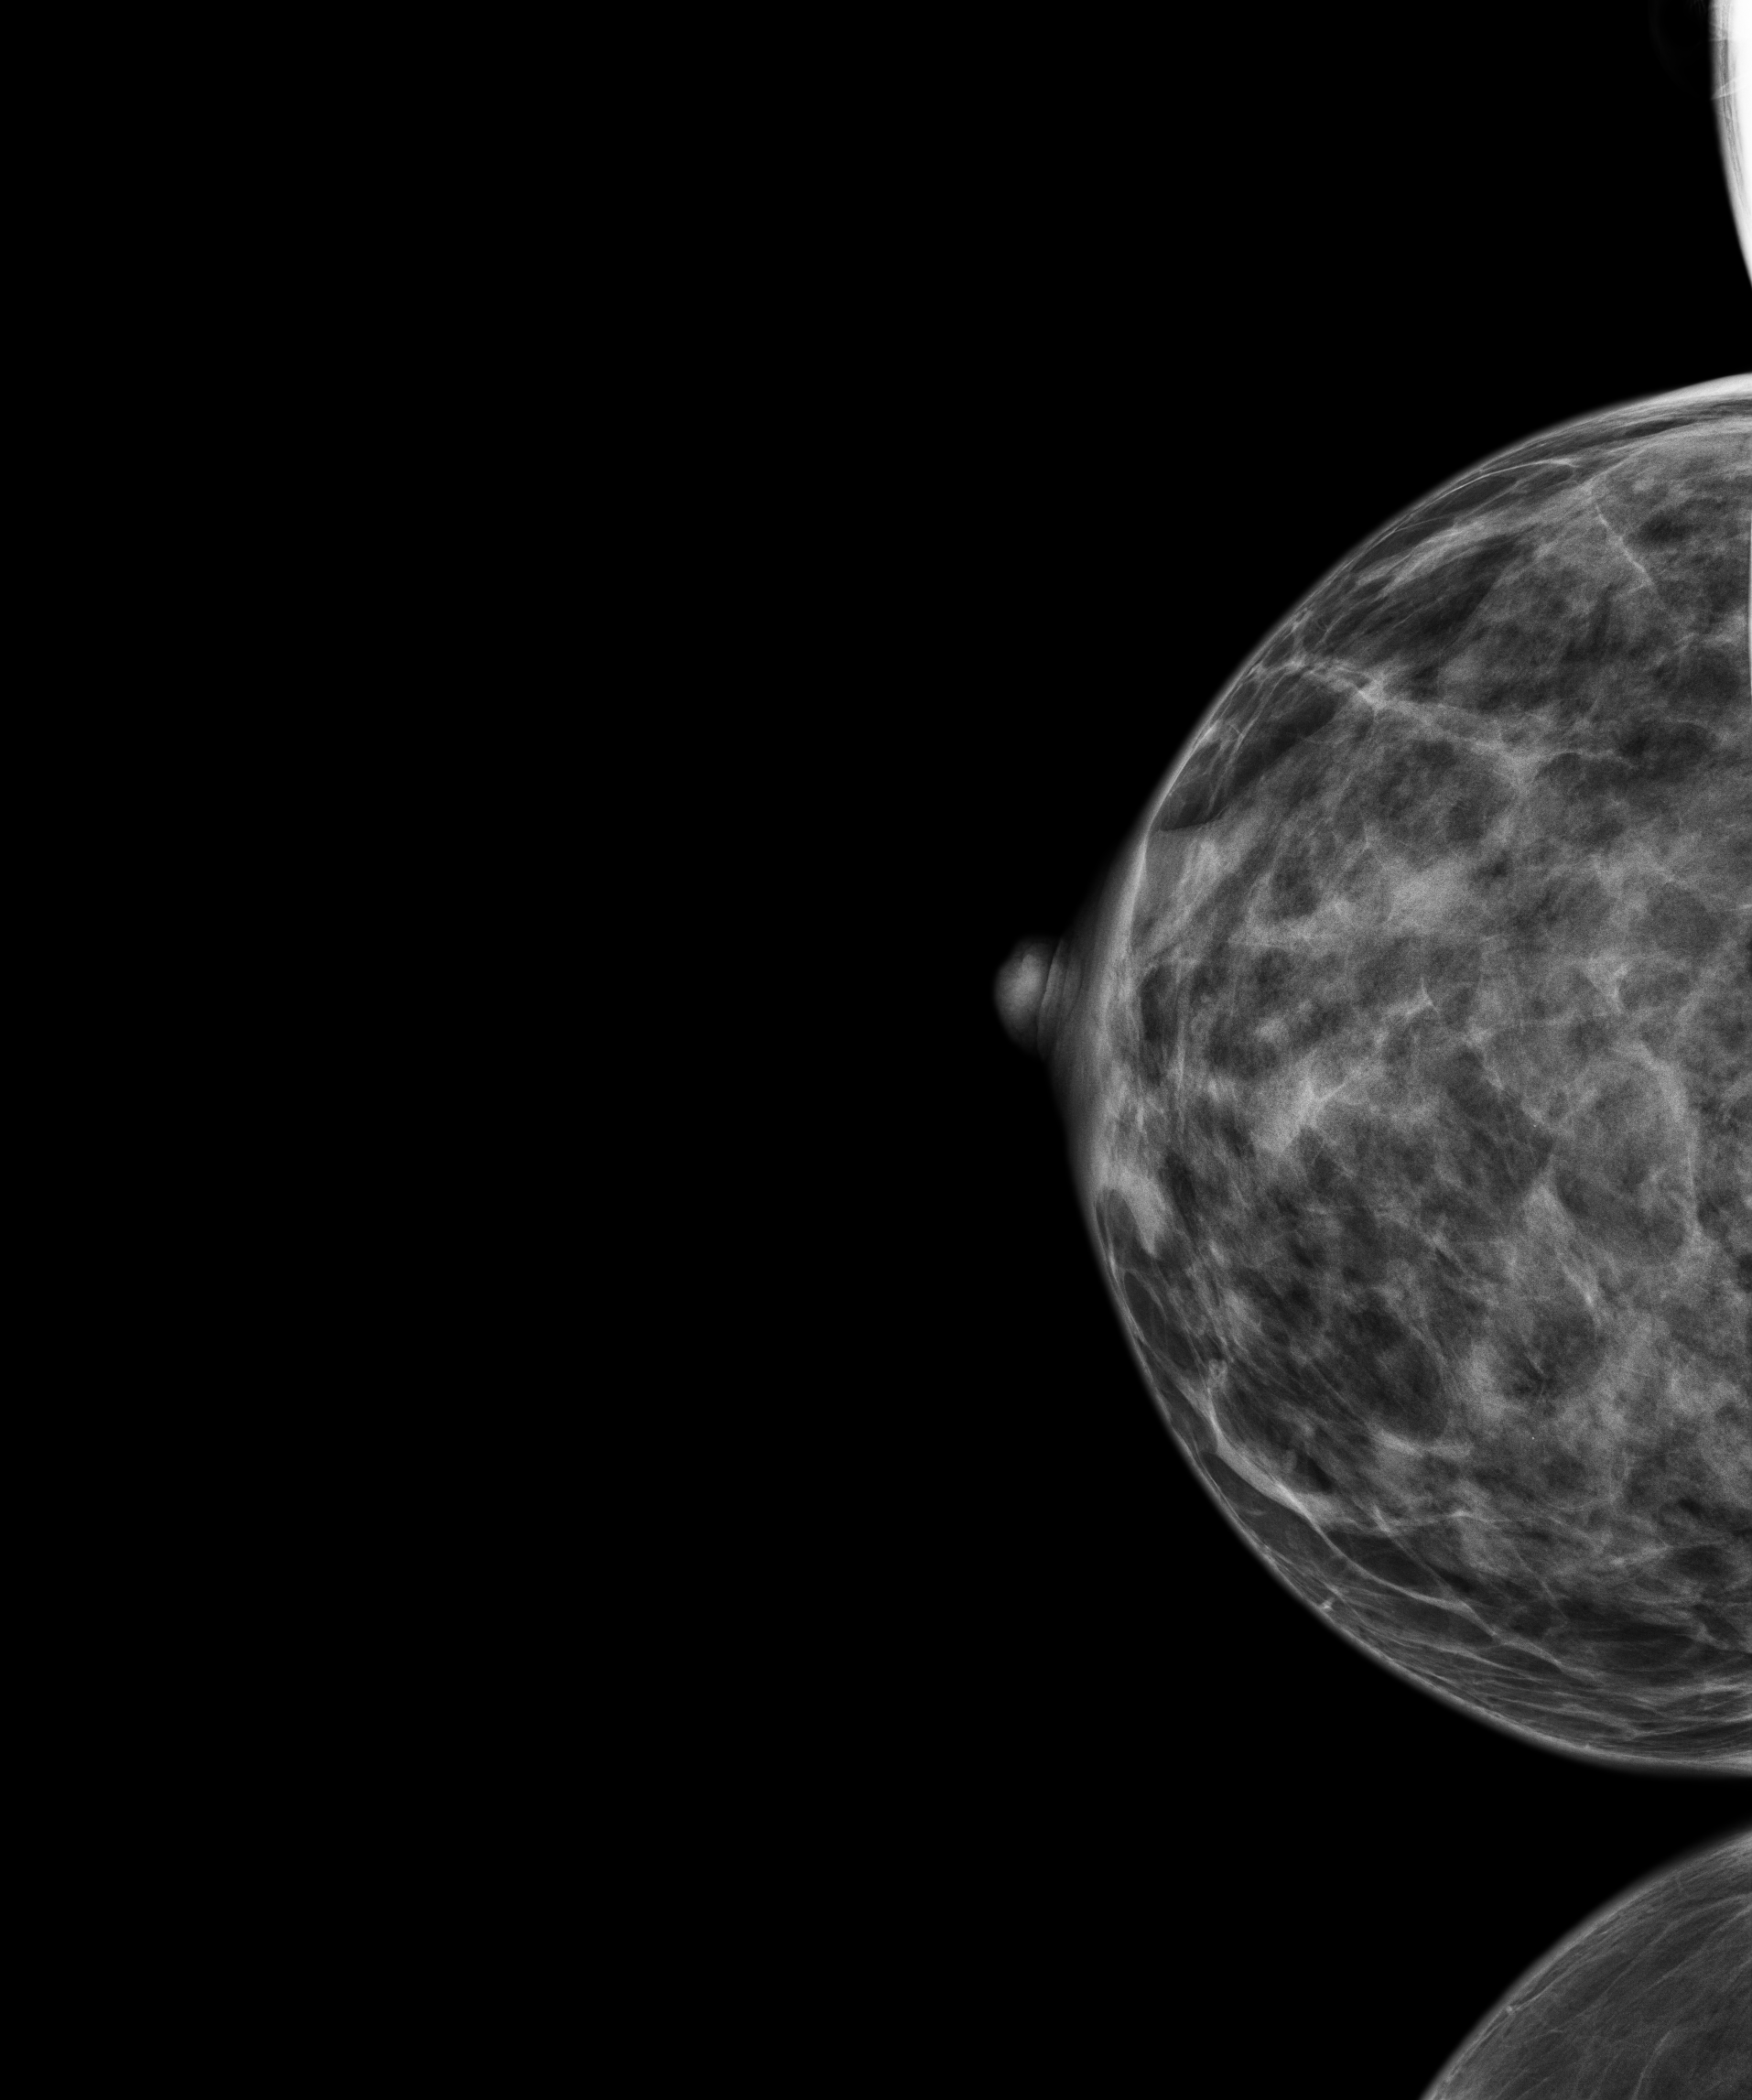
Full-field digital mammogram (FFDM); right breast; CC view; screening examination. Patient aged 45 years (female).
Breast density at the screening exam (both breasts): heterogeneously dense (BI-RADS density category c). Final BI-RADS category for the screening round (tomosynthesis exam, both breasts): category 1. Recall: no recall after this screen.